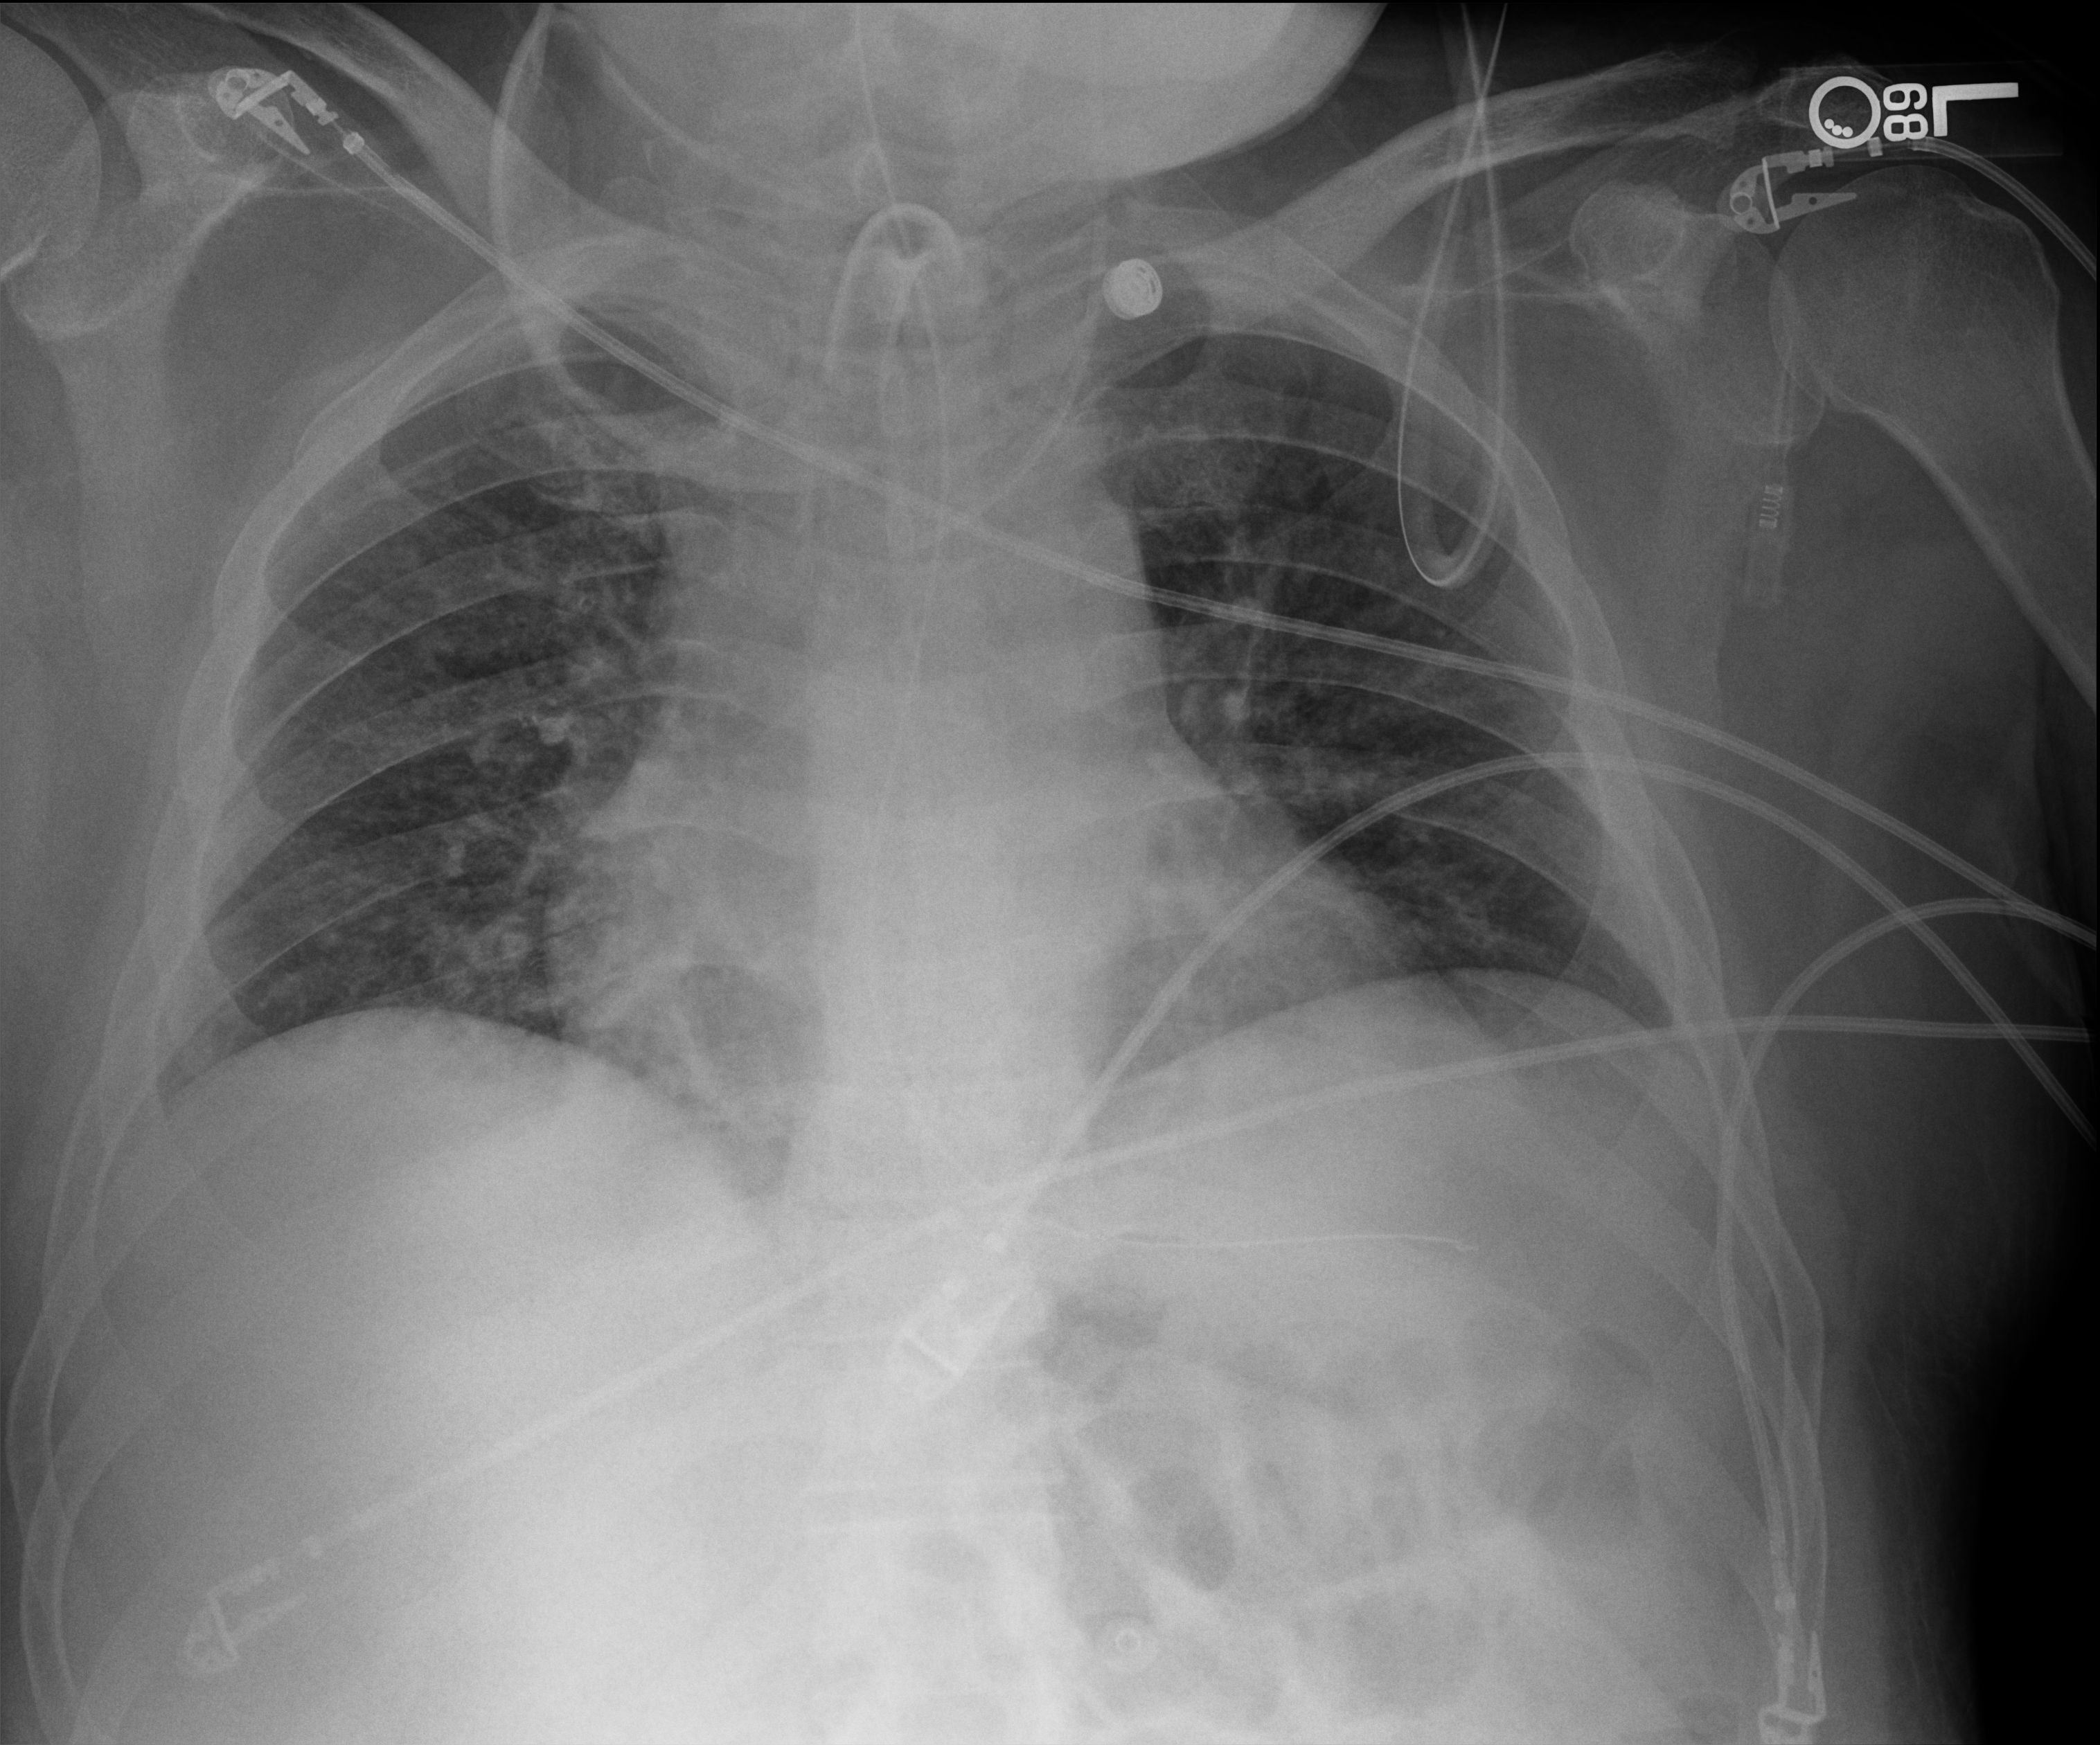
Portable chest radiograph; anteroposterior (AP) projection. Male patient hospitalised with COVID-19, age 18–59 years.
From the hospital-stay record, not from the radiograph (when in the stay this image was taken is not recorded): length of hospital stay: 65 days.